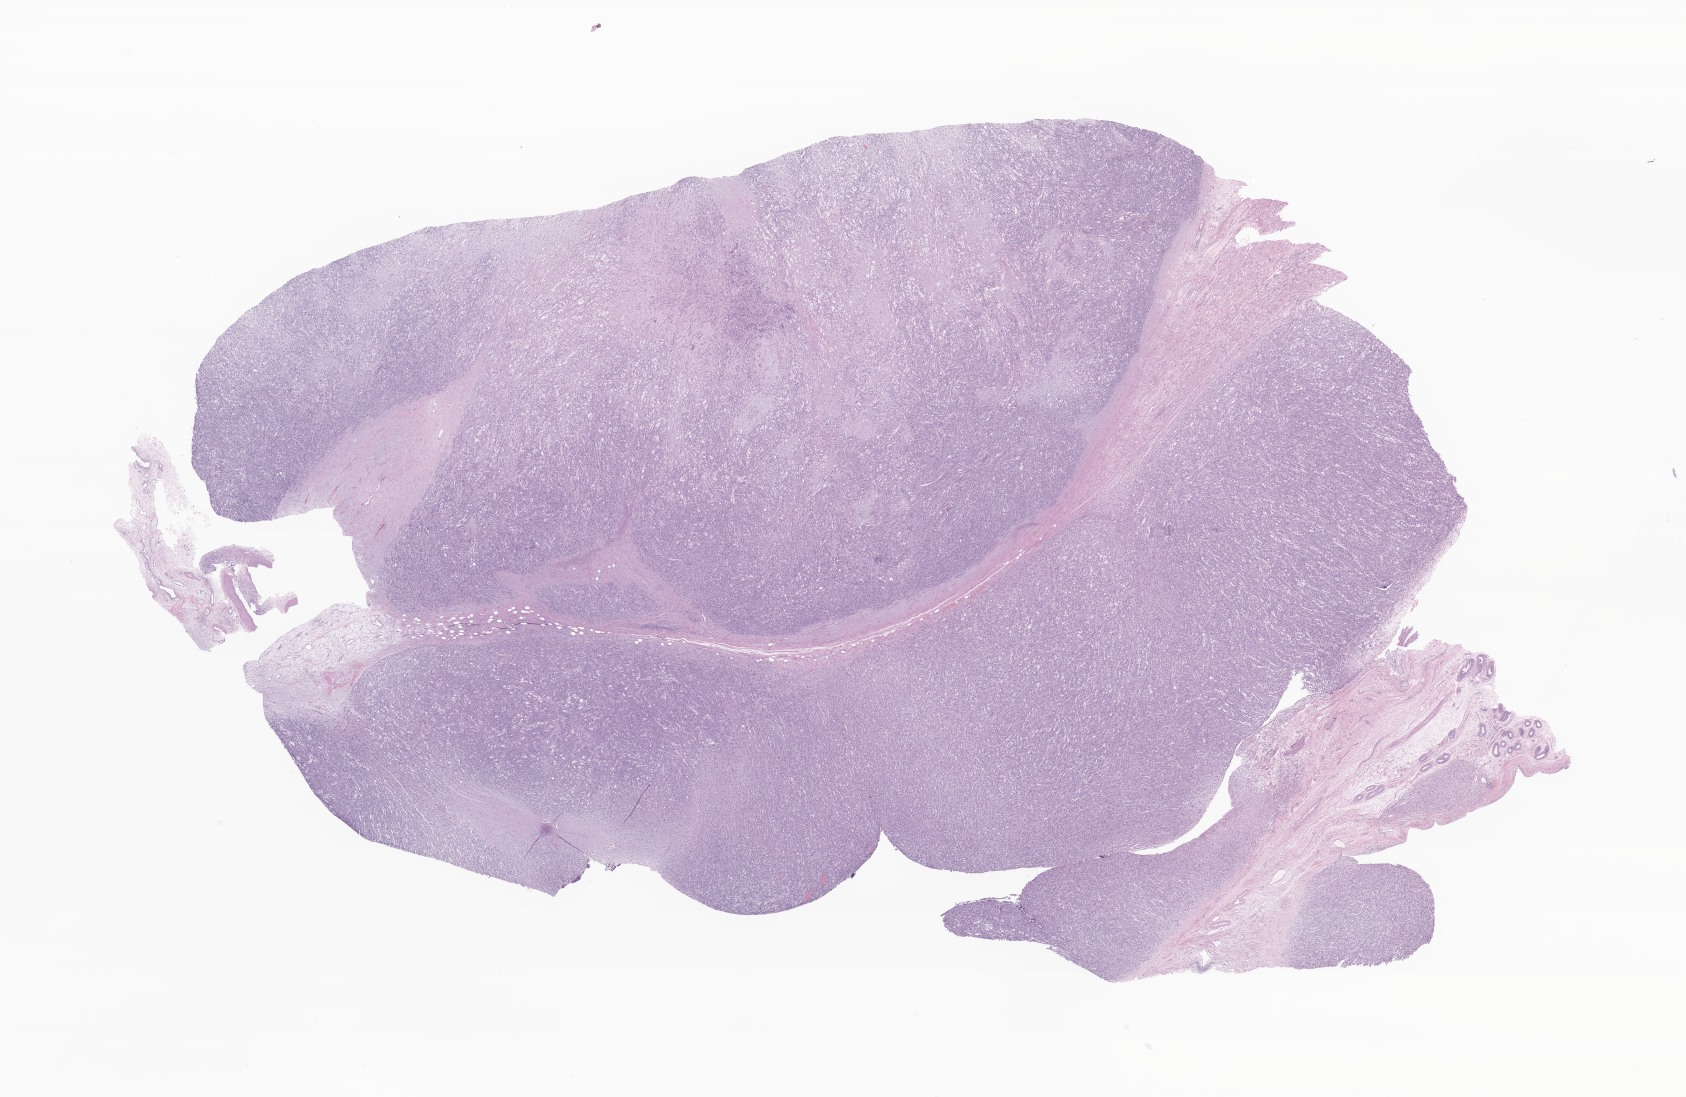
Haematoxylin and eosin whole-slide image of tumor tissue from the testis, shown as a low-resolution overview of the whole scanned area (about 28.4 x 18.5 mm). Formalin-fixed paraffin-embedded section. Patient male; age 156 months (13 years).
• diagnosis (ICD-O-3 morphology term): Rhabdomyosarcoma, NOS